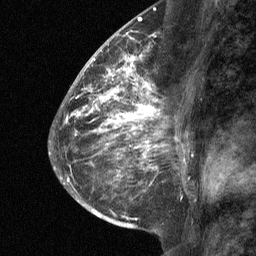
Breast MRI (dynamic contrast-enhanced), one sagittal slice; position 35 of 64 along the scan axis; dynamic contrast-enhanced study with each time point stored as its own series, time point 2 of 3 at this slice position (early post-contrast, ordered by acquisition time); 1.5 T; TE 4.8 ms, TR 27 ms; 256 × 256 image matrix, field of view 180 × 180 mm. Female patient, age 59 years. From the clinical record (not read from this slice): setting: breast cancer imaged before/during neoadjuvant chemotherapy; receptor status: triple-negative.
Annotated regions visible in this slice (semi-automatically segmented with operator editing):
- analysis volume of interest (the breast-tissue region the enhancement analysis was run in; not a lesion): box from (x=122, y=58) to (x=172, y=109) px
- tumour enhancement mask (voxels above the 90 % enhancement threshold inside the analysis volume of interest): (x=122, y=58)–(x=162, y=109)